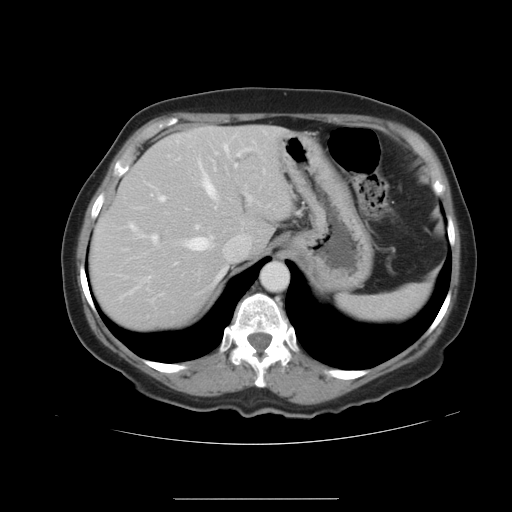
Contrast-enhanced abdominal CT, one axial slice. Slice 29 of 41 in the series (ordered by position). 120 kVp. Intravenous contrast given. Soft-tissue window (W 400 / L 40 HU). 5 mm slice thickness. 512 × 512 image matrix. Female patient, age 63 years. From the clinical record (not read from this slice): diagnosis: colorectal cancer liver metastases, imaged before liver resection; multiple liver metastases: yes; largest metastasis: 1.5 cm; disease in both lobes: yes.
Outlined on this slice (manually delineated by an expert):
- hepatic veins: bounding box <124,141,236,295> (left, top, right, bottom; pixels)
- liver: <91,126,293,331>
- planned liver remnant (the part of the liver to remain after resection): <91,126,293,331>
- portal vein (with intrahepatic branches): <152,148,248,240>